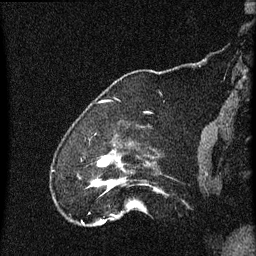
Breast MRI (dynamic contrast-enhanced), one sagittal slice; slice 12 of 60 in the series (ordered by position); dynamic contrast-enhanced series, image 2 of 4 at this slice position (ordered by acquisition); 1.5 T; TE 4.2 ms, TR 8 ms; 2 mm slice thickness; 256 × 256 image matrix, field of view 180 × 180 mm. Patient: female, 52 years.
Outlined on this slice (semi-automatically segmented with operator editing):
- analysis volume of interest (the breast-tissue region the enhancement analysis was run in; not a lesion): bounding box <77,150,164,219> (left, top, right, bottom; pixels)
- tumour enhancement mask (voxels above the 70 % enhancement threshold inside the analysis volume of interest): <93,158,115,187>